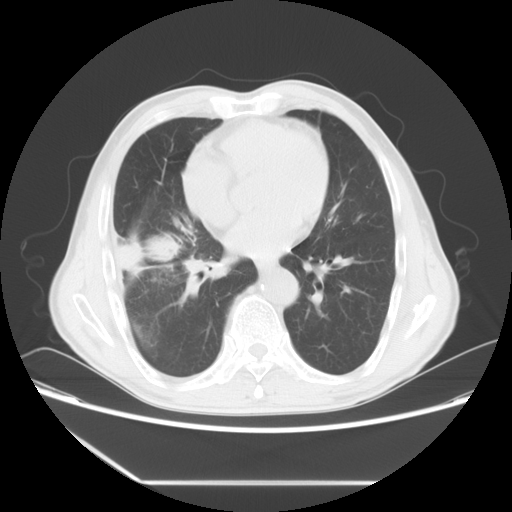
Chest CT, one axial slice. Position 26 of 60 along the scan axis. 120 kVp. Lung window (W 1500 / L -600 HU). 512 × 512 image matrix, field of view 386 × 386 mm. Patient: male, 72 years. Case-level facts recorded for this patient, not image findings: clinical TNM (as recorded): T1c N0 M0.
Outlined on this slice (bounding box drawn by a radiologist):
- lung tumour (recorded histology: squamous cell carcinoma): bounding box [x1, y1, x2, y2] px = [112, 220, 201, 300]